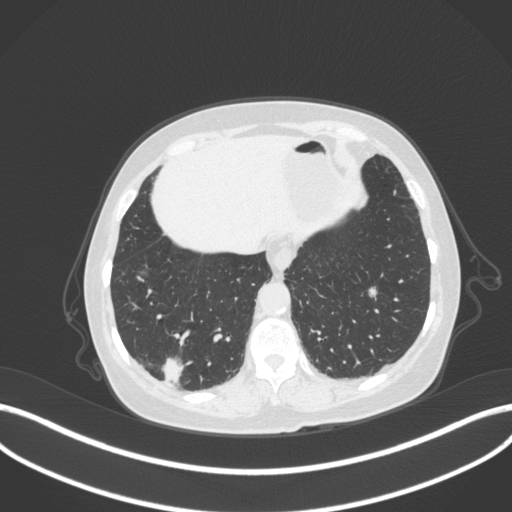
Chest CT, one axial slice. Slice 63 of 340 in the series (ordered by position). Reconstruction kernel B31f. 120 kVp. Lung window (W 1500 / L -600 HU). 1 mm slice thickness. 512 × 512 image matrix, field of view 400 × 400 mm. Female patient, age 69 years. From the clinical record (not read from this slice): clinical TNM (as recorded): T1b N0 M0; histopathological grade: G2-3.
Outlined on this slice (rectangle marked by the reading radiologist):
- lung tumour (recorded histology: adenocarcinoma): box from (x=158, y=353) to (x=185, y=384) px